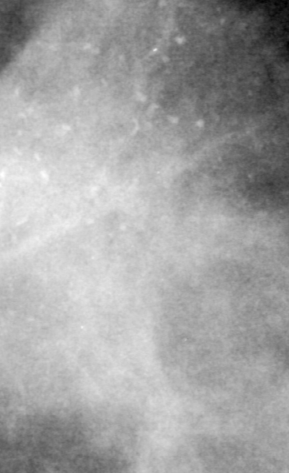
Cropped region of a digitized screen-film mammogram centred on a radiologist-marked abnormality, right breast, CC view.
Finding: calcifications, morphology pleomorphic, distribution clustered; BI-RADS assessment category 4; subtlety rating 4 on a 1 (subtle) to 5 (obvious) scale; pathology result (as recorded, not read from the image): malignant.